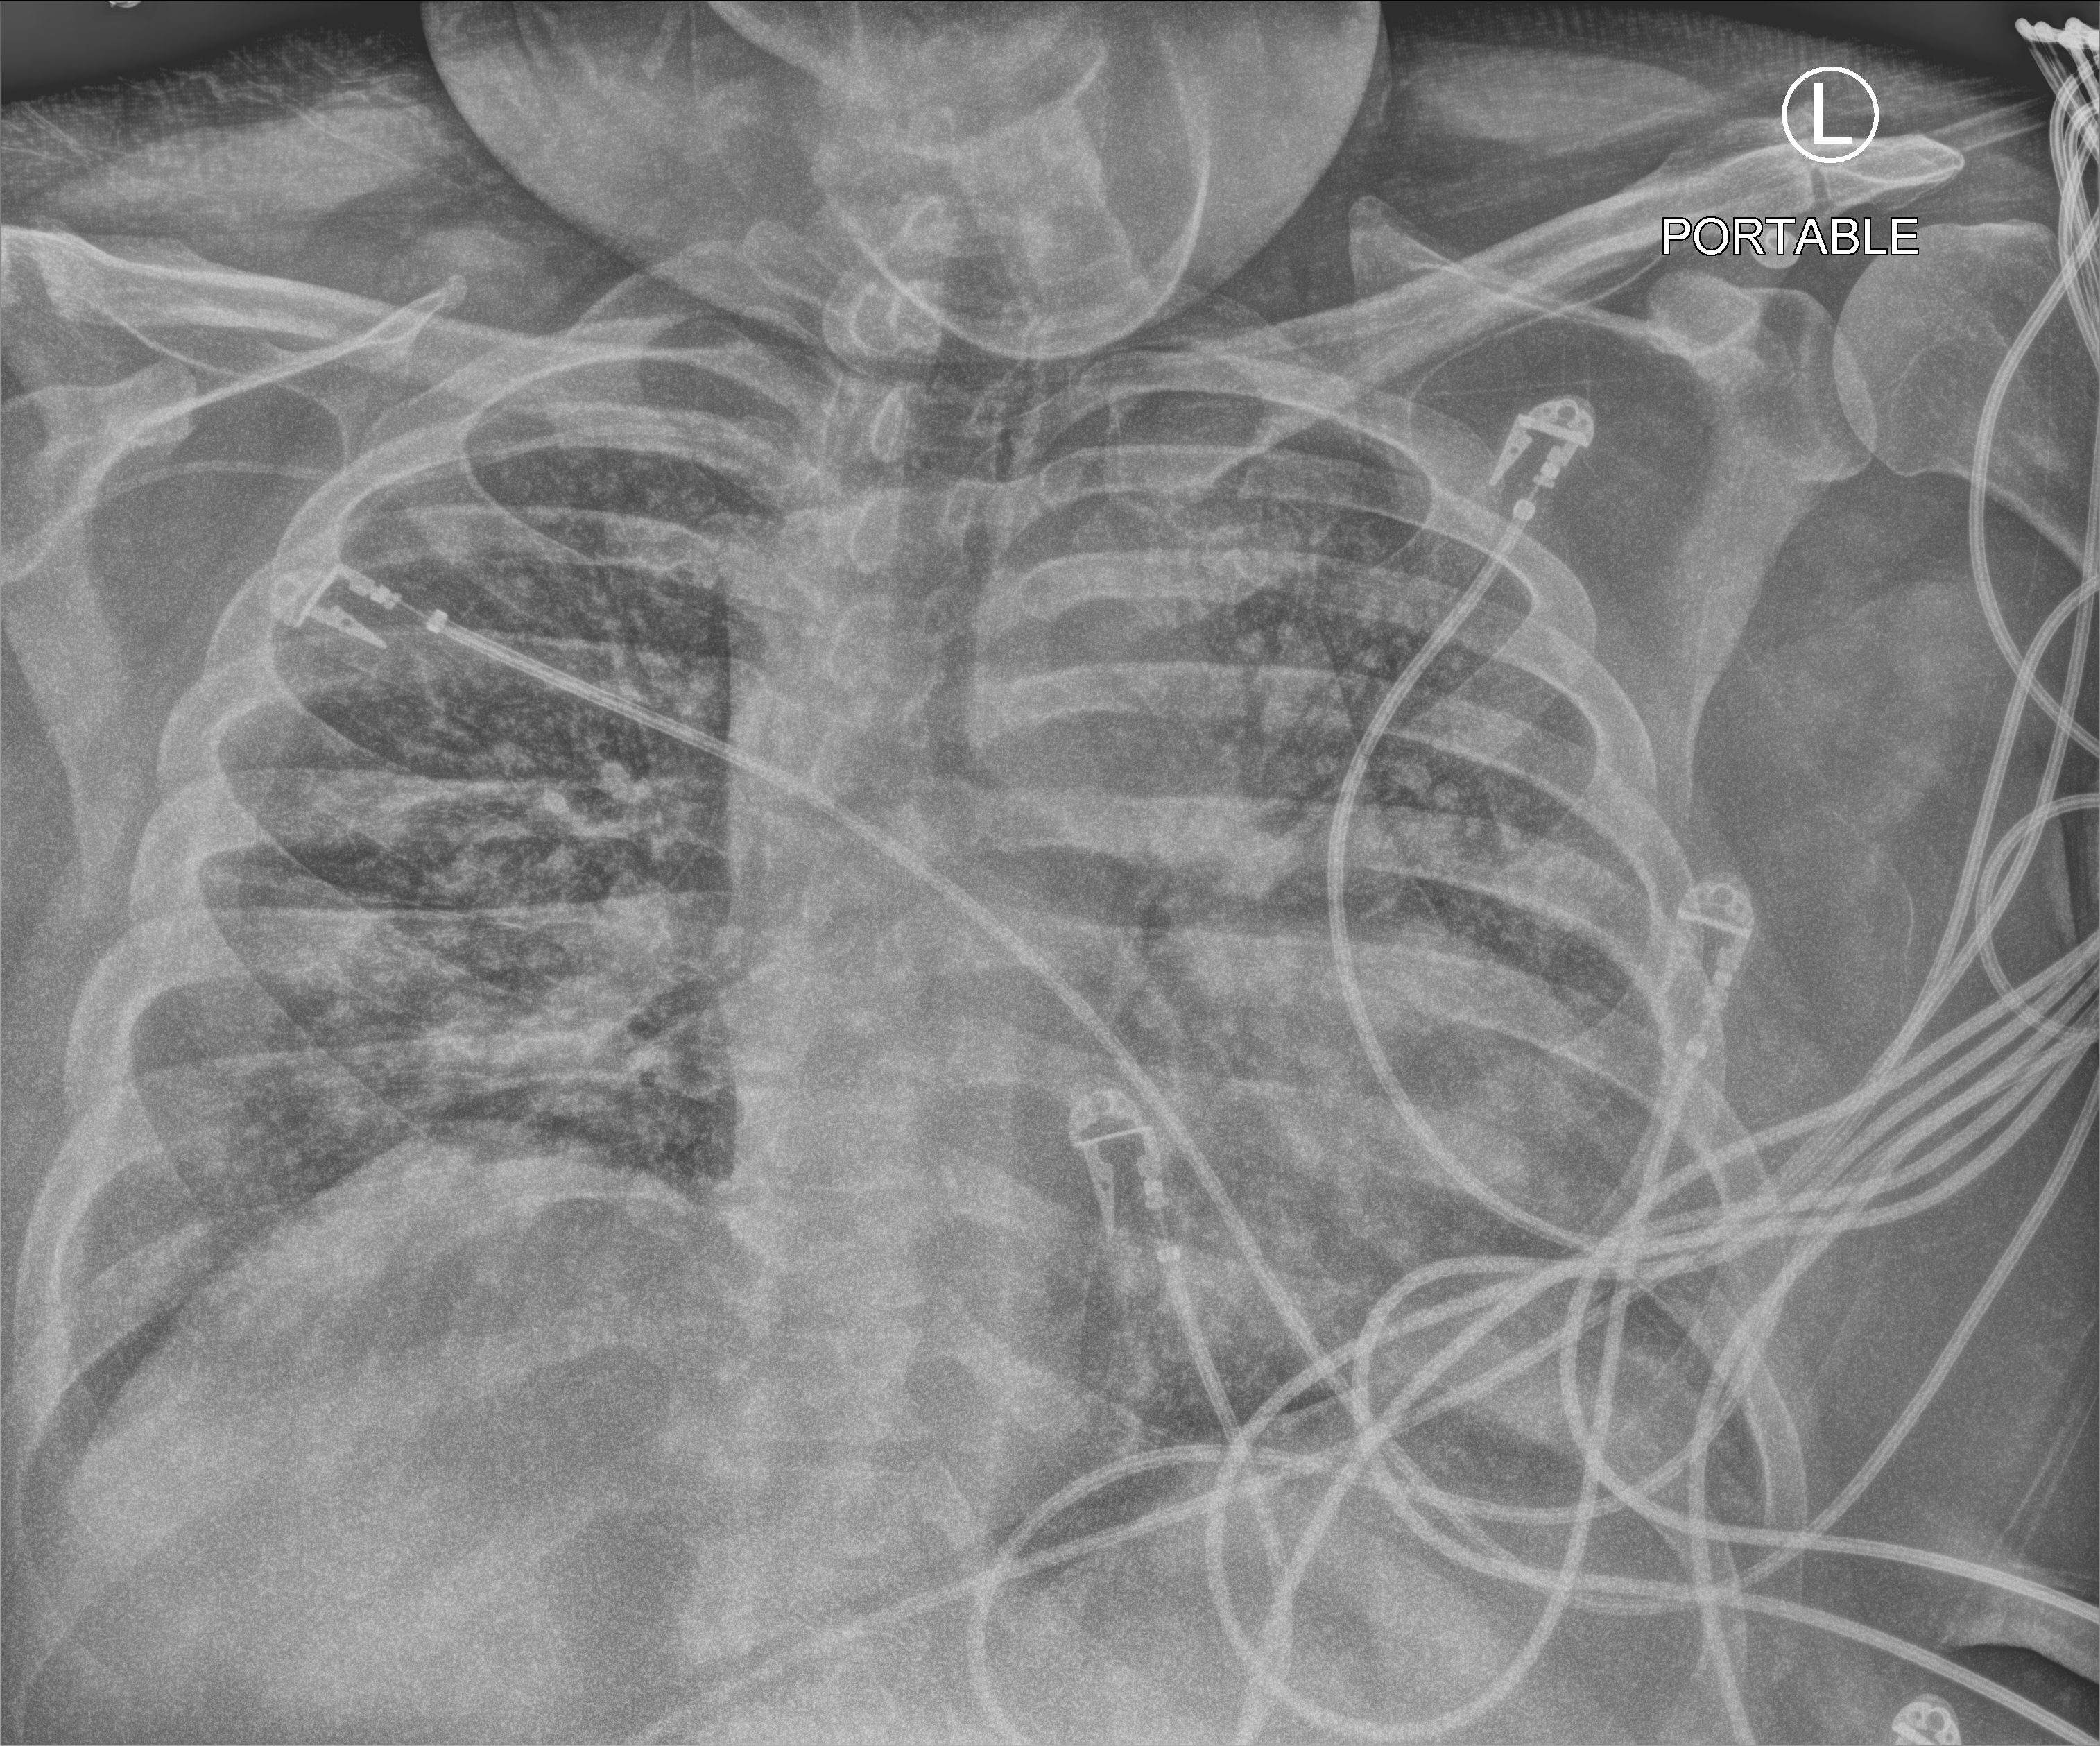
Bedside chest radiograph (computed radiography); anteroposterior (AP) projection. Adult patient hospitalised with COVID-19, age 18–59 years.
Hospital-stay facts (about this admission, not read from this image; timing relative to this image not recorded):
- hypertension (admission record): yes
- diabetes (admission record): yes